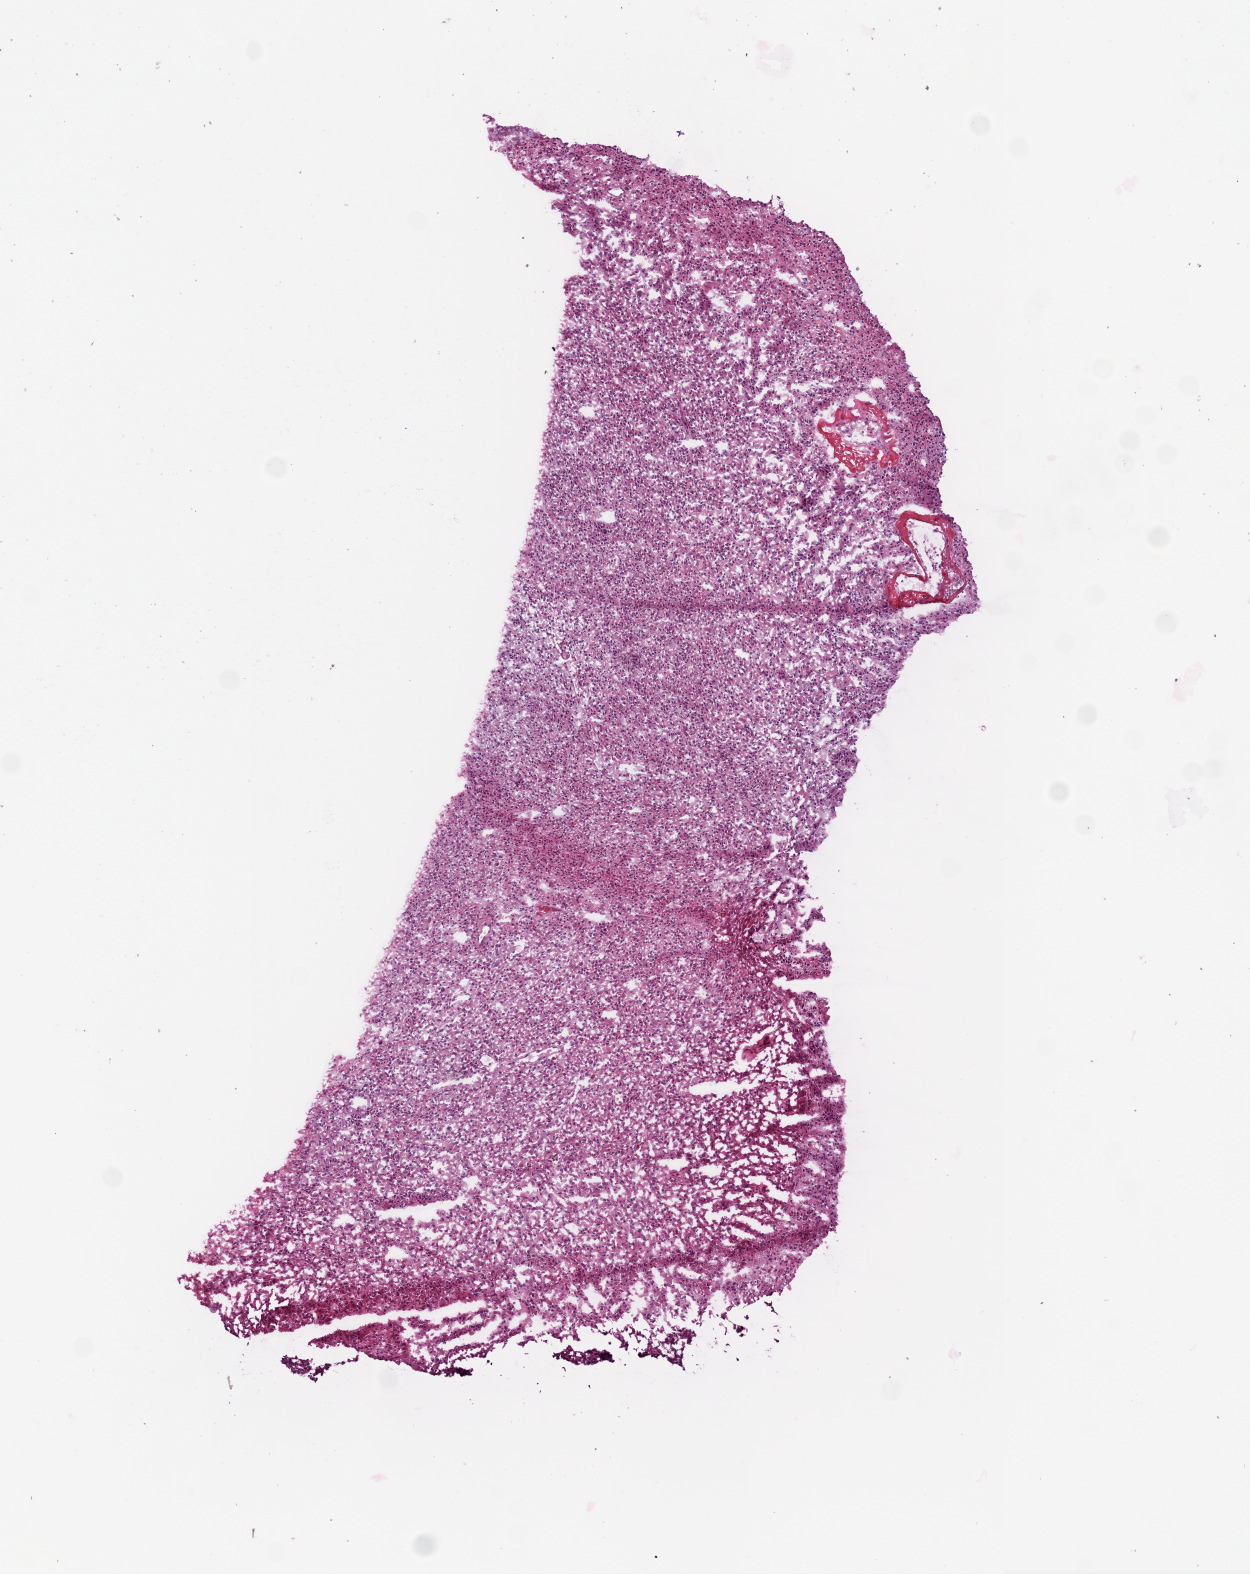
Whole-slide histology image, Hematoxylin and eosin (H&E) stained, a low-resolution overview of the entire scanned area, about 5.0 x 6.3 mm, frozen section from the bottom of the tissue portion, brain, primary tumour sample. Male, age 59 years at initial diagnosis. Slide review estimates, as recorded: tumour cells 100%, tumour nuclei 80%, normal cells 0%, stromal cells 0%, necrosis 0%.
Pathologic diagnosis: Glioblastoma.